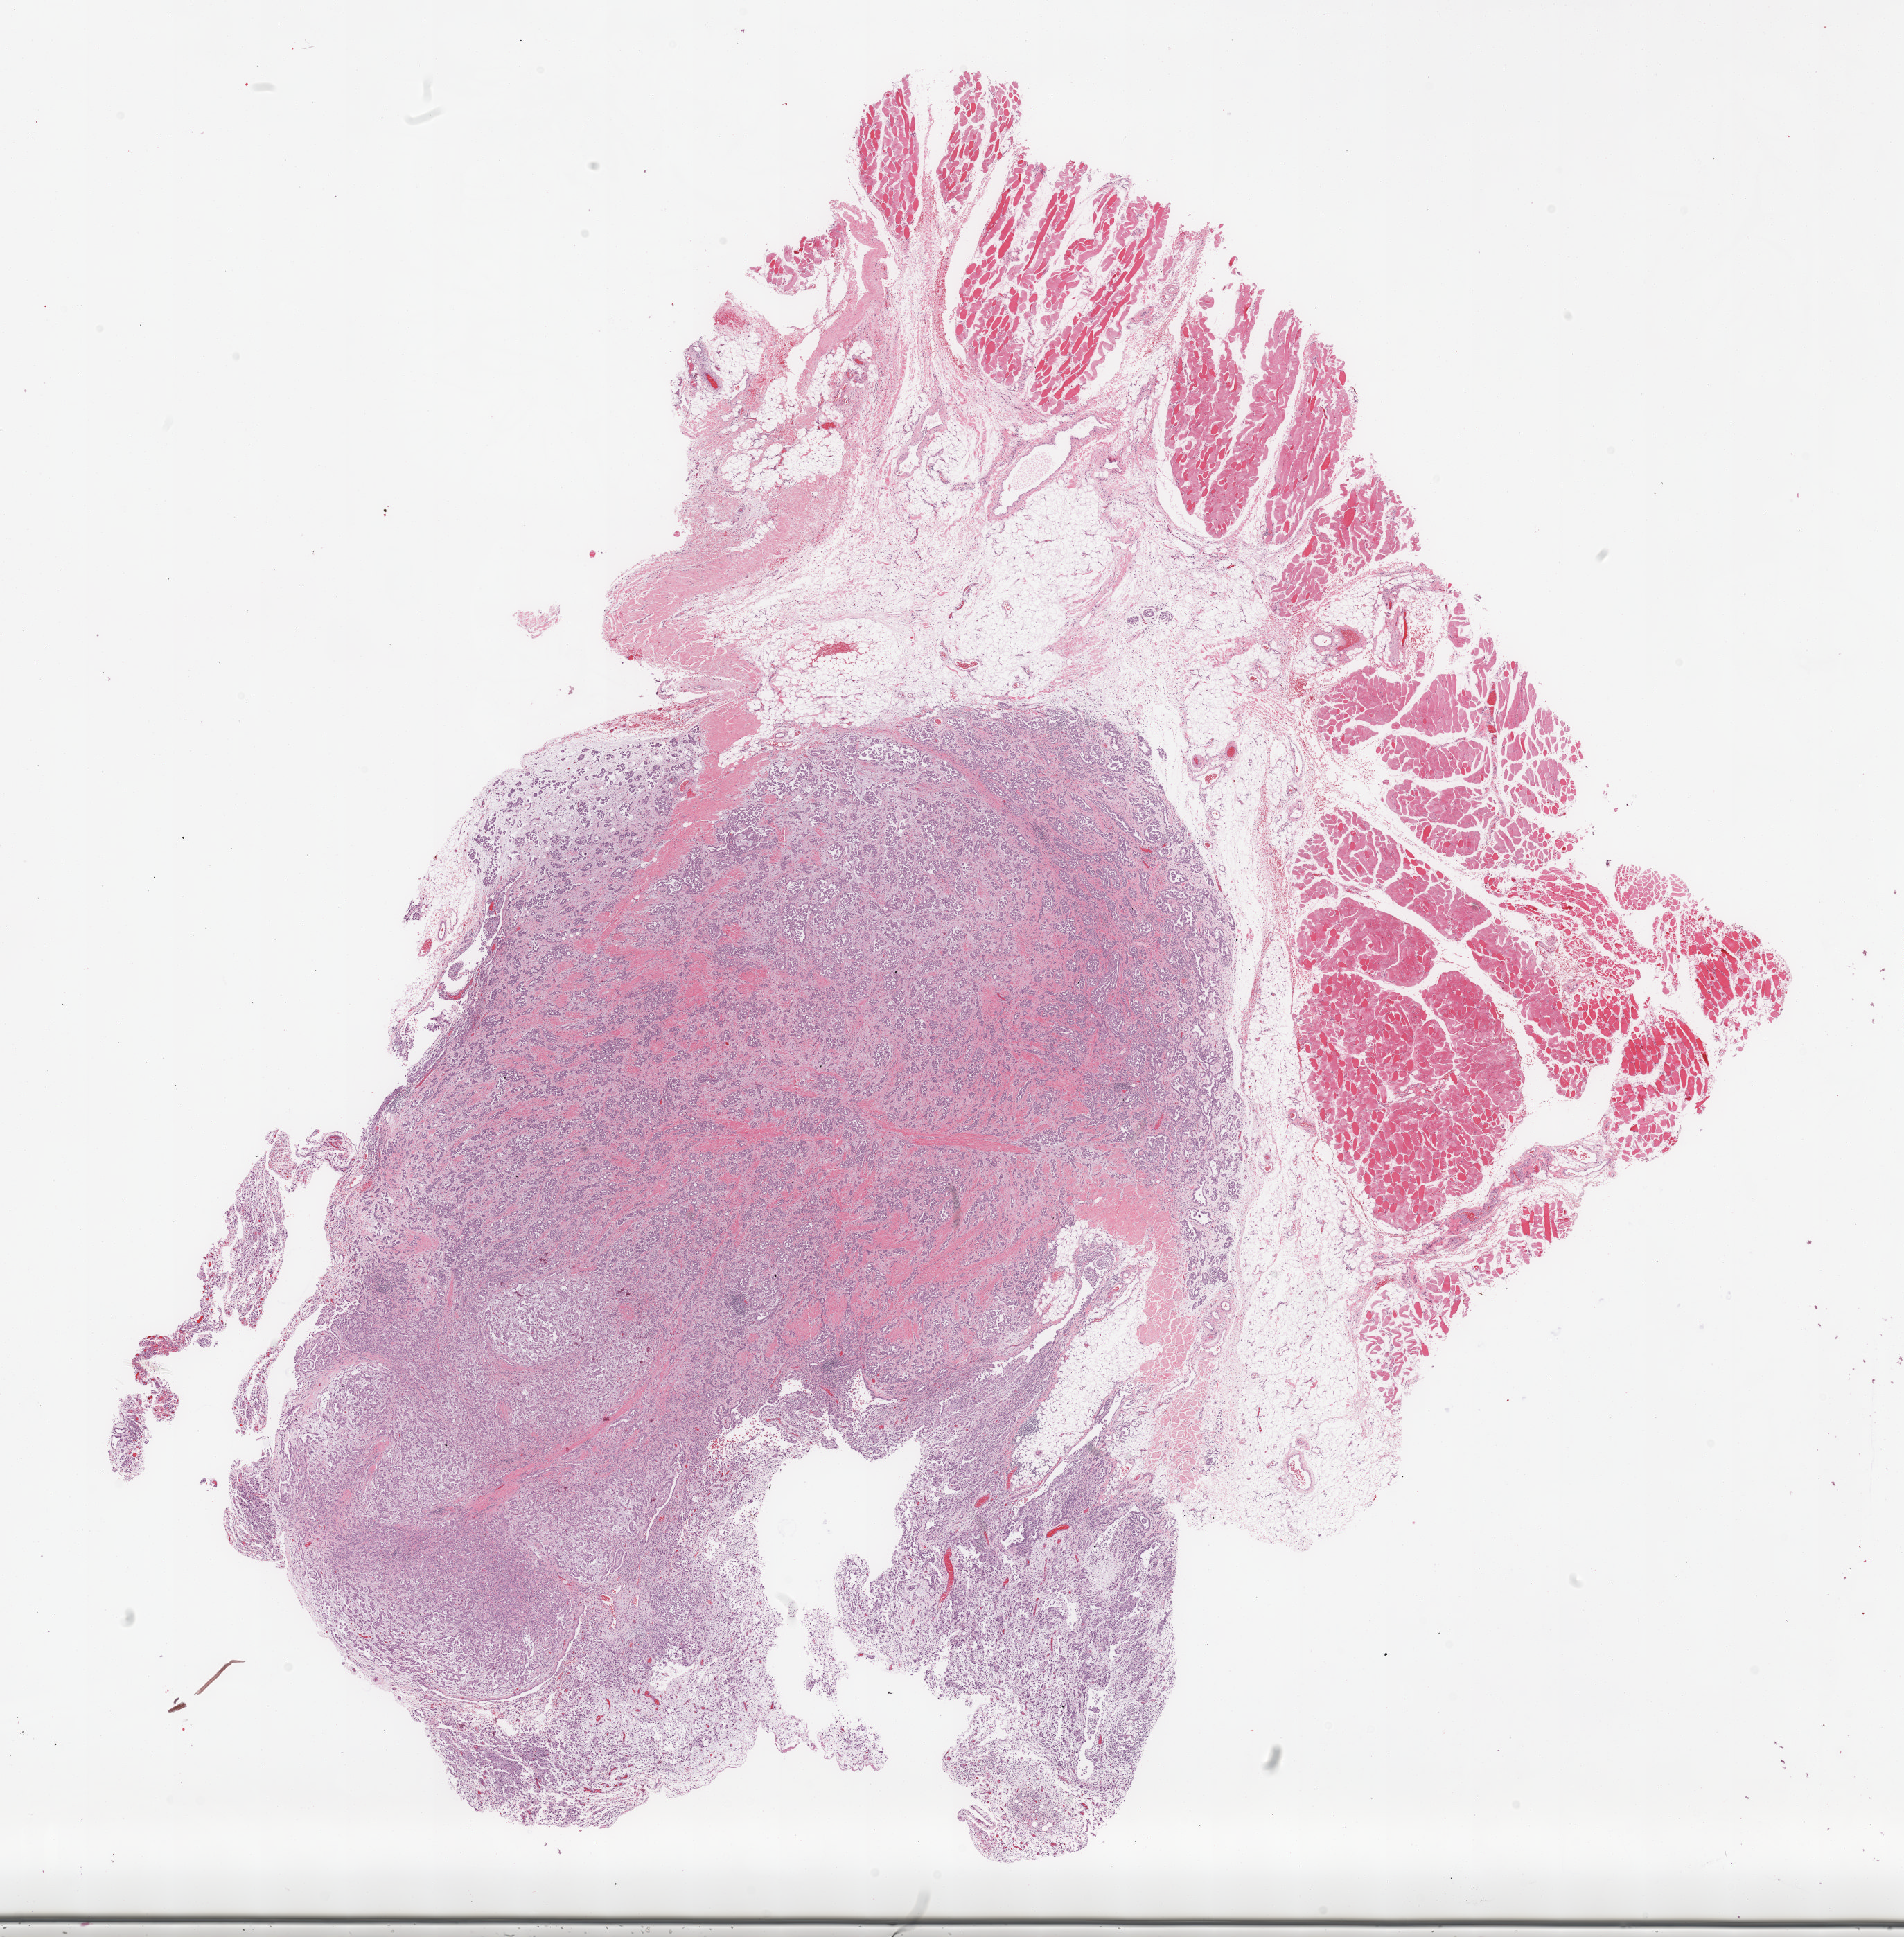
Hematoxylin and eosin (H&E) stained whole-slide image — whole scanned area (about 22.1 x 22.4 mm, slide scanned at 20x) shown as a low-resolution overview, formalin-fixed paraffin-embedded (FFPE) diagnostic section, primary tumour sample from the mesothelium. Patient: female, age at initial diagnosis 60 years.
AJCC pathologic stage: III. Pathologic diagnosis: Epithelioid mesothelioma, malignant (pleura, NOS).